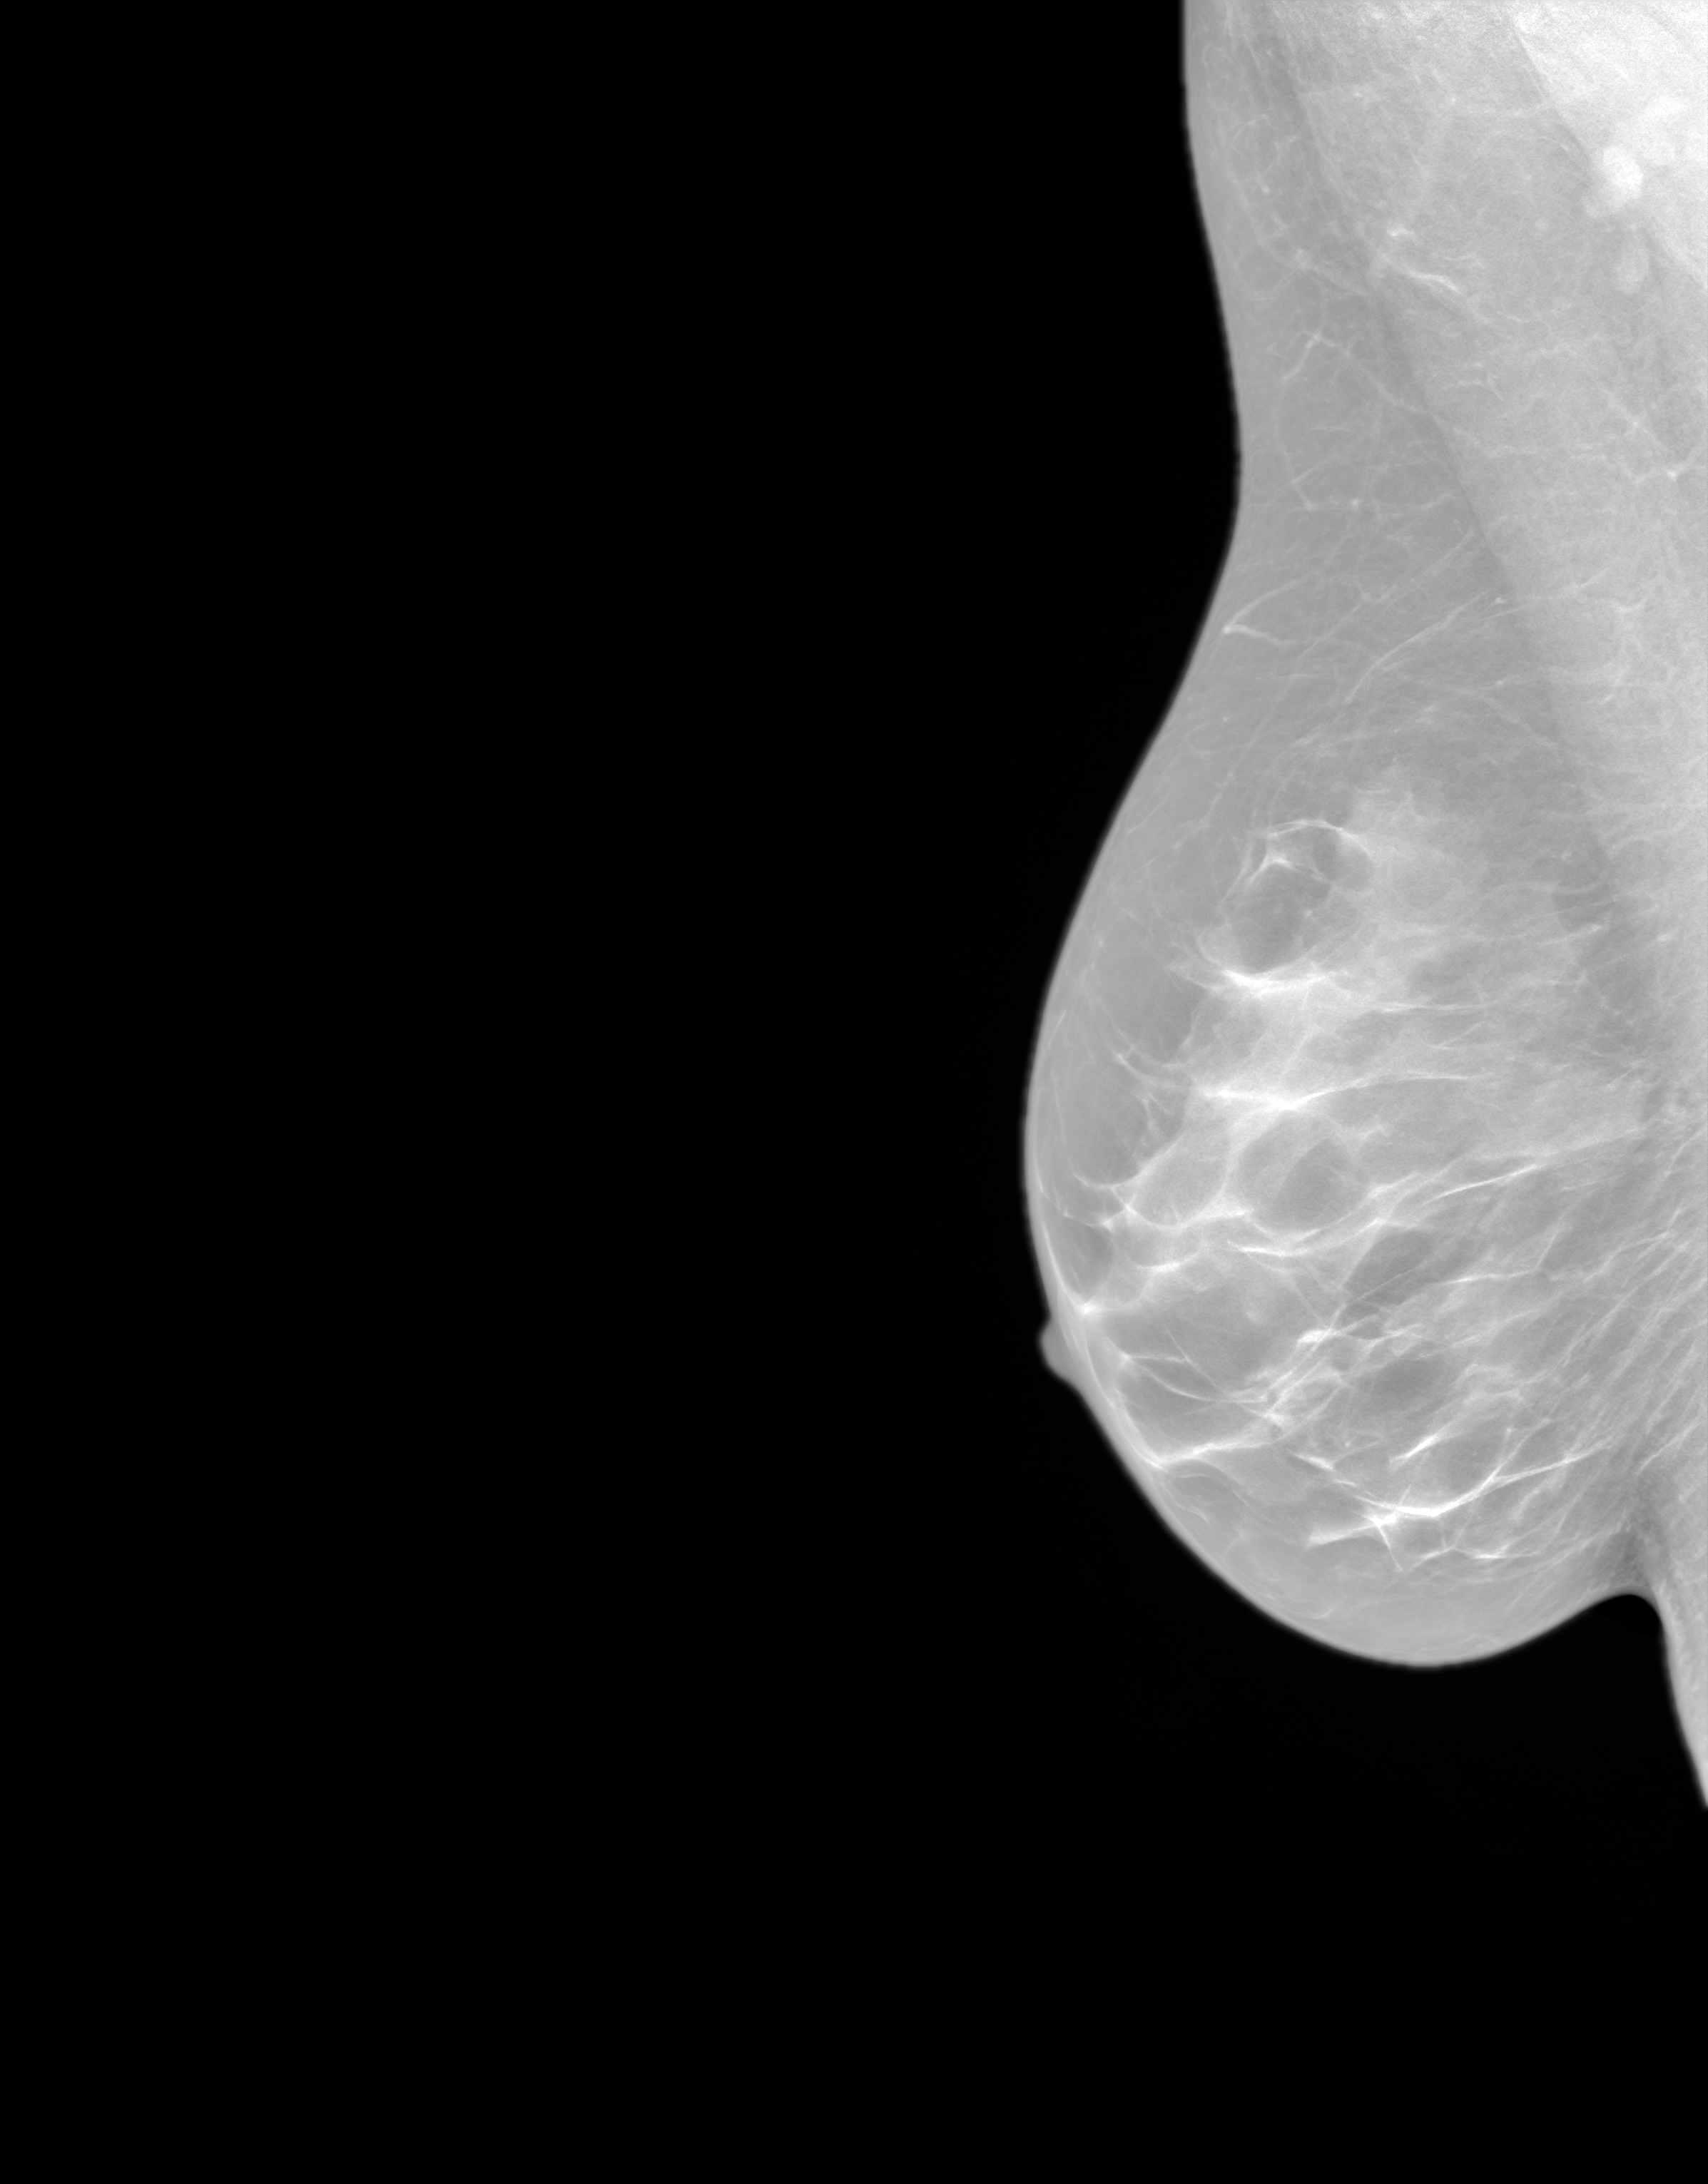
Synthetic 2-D view generated from a tomosynthesis acquisition (not an FFDM exposure), right breast, medio-lateral oblique projection, annual screening mammography examination. Patient aged 51 years (female).
Breast density at the screening exam (both breasts): heterogeneously dense (BI-RADS density category c). Final BI-RADS category for the screening round (tomosynthesis exam, both breasts): category 1. Recall: no recall after this screen.